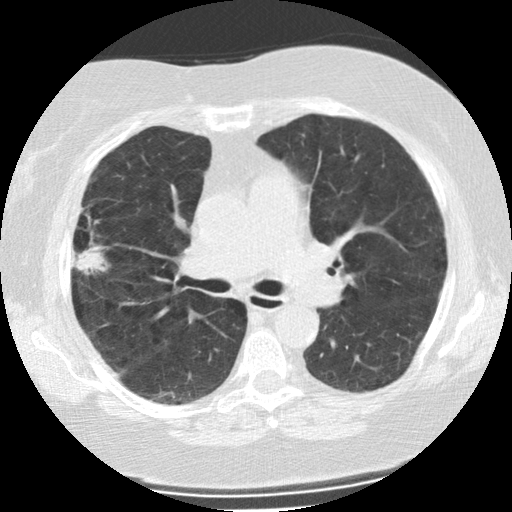
Low-dose screening chest CT, one axial slice; slice 140 of 225 in the series (ordered by position); reconstruction kernel STANDARD; lung window (W 1500 / L -600 HU); 512 × 512 image matrix, field of view 320 × 320 mm.
Structures marked on this image (outlined manually by an expert reader):
- lesion 1 (tumor, upper lobe of right lung): bounding box <73,242,109,275> (left, top, right, bottom; pixels)